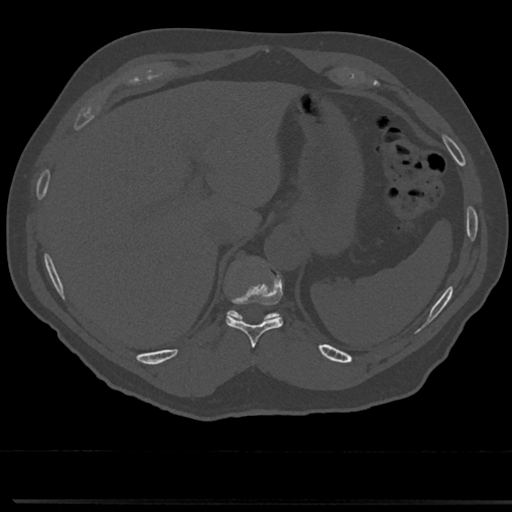
CT including the spine, one axial slice; slice 243 of 817 in the series (ordered by position); bone window (W 1800 / L 400 HU); 0.5 mm slice thickness; 512 × 512 image matrix. Male patient, age 61 years. Case-level facts recorded for this patient, not image findings: primary cancer: prostate.
Structures marked on this image (semi-automatically segmented with operator editing):
- T10 vertebra: bounding box (x1, y1, x2, y2) in pixels: (224, 257, 284, 345)
- T11 vertebra: (229, 313, 277, 321)